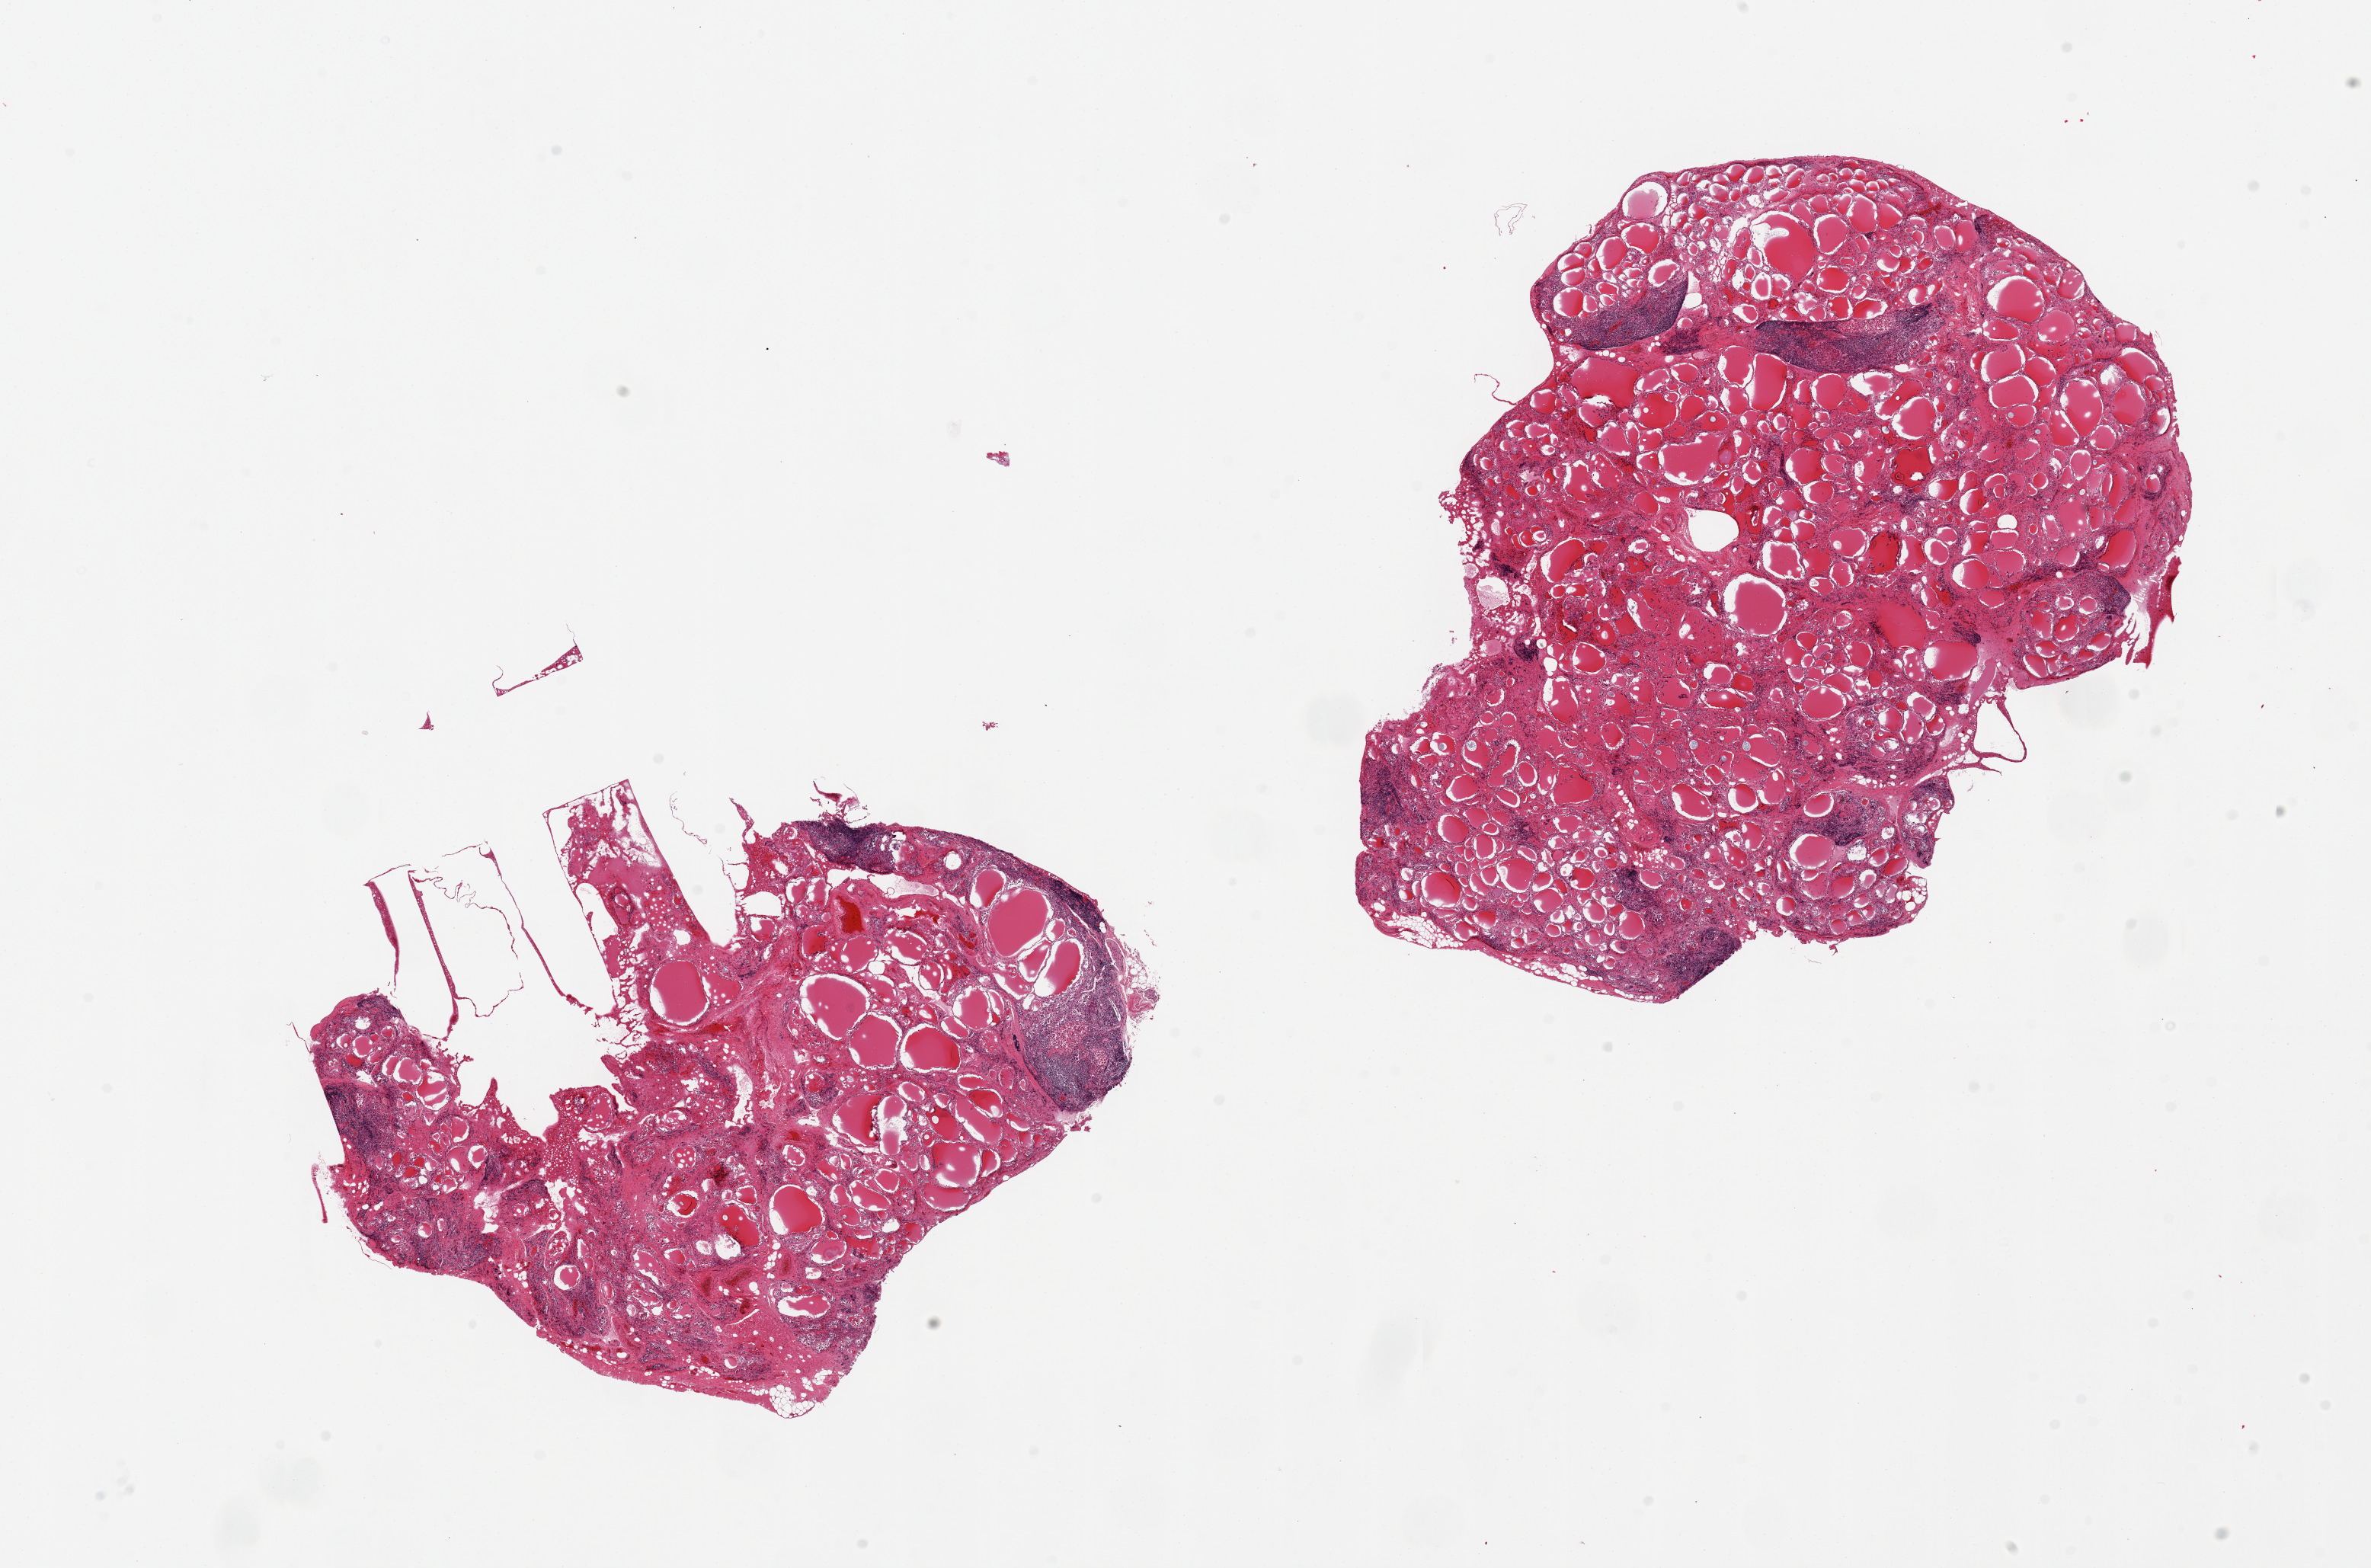
Digitized haematoxylin and eosin-stained section, brightfield — a low-resolution overview of the entire scanned area, about 24.6 x 16.3 mm (acquisition: 20x scan), PAXgene-fixed, paraffin-embedded tissue, section of thyroid (target tissue), donor tissue sample. Donor sex: male.
• pathologist's review note for this sample: 2 pieces, mulitple lymphoid aggregates consistent with Hashimoto's thyroiditis; regressive/fibrotic areas present